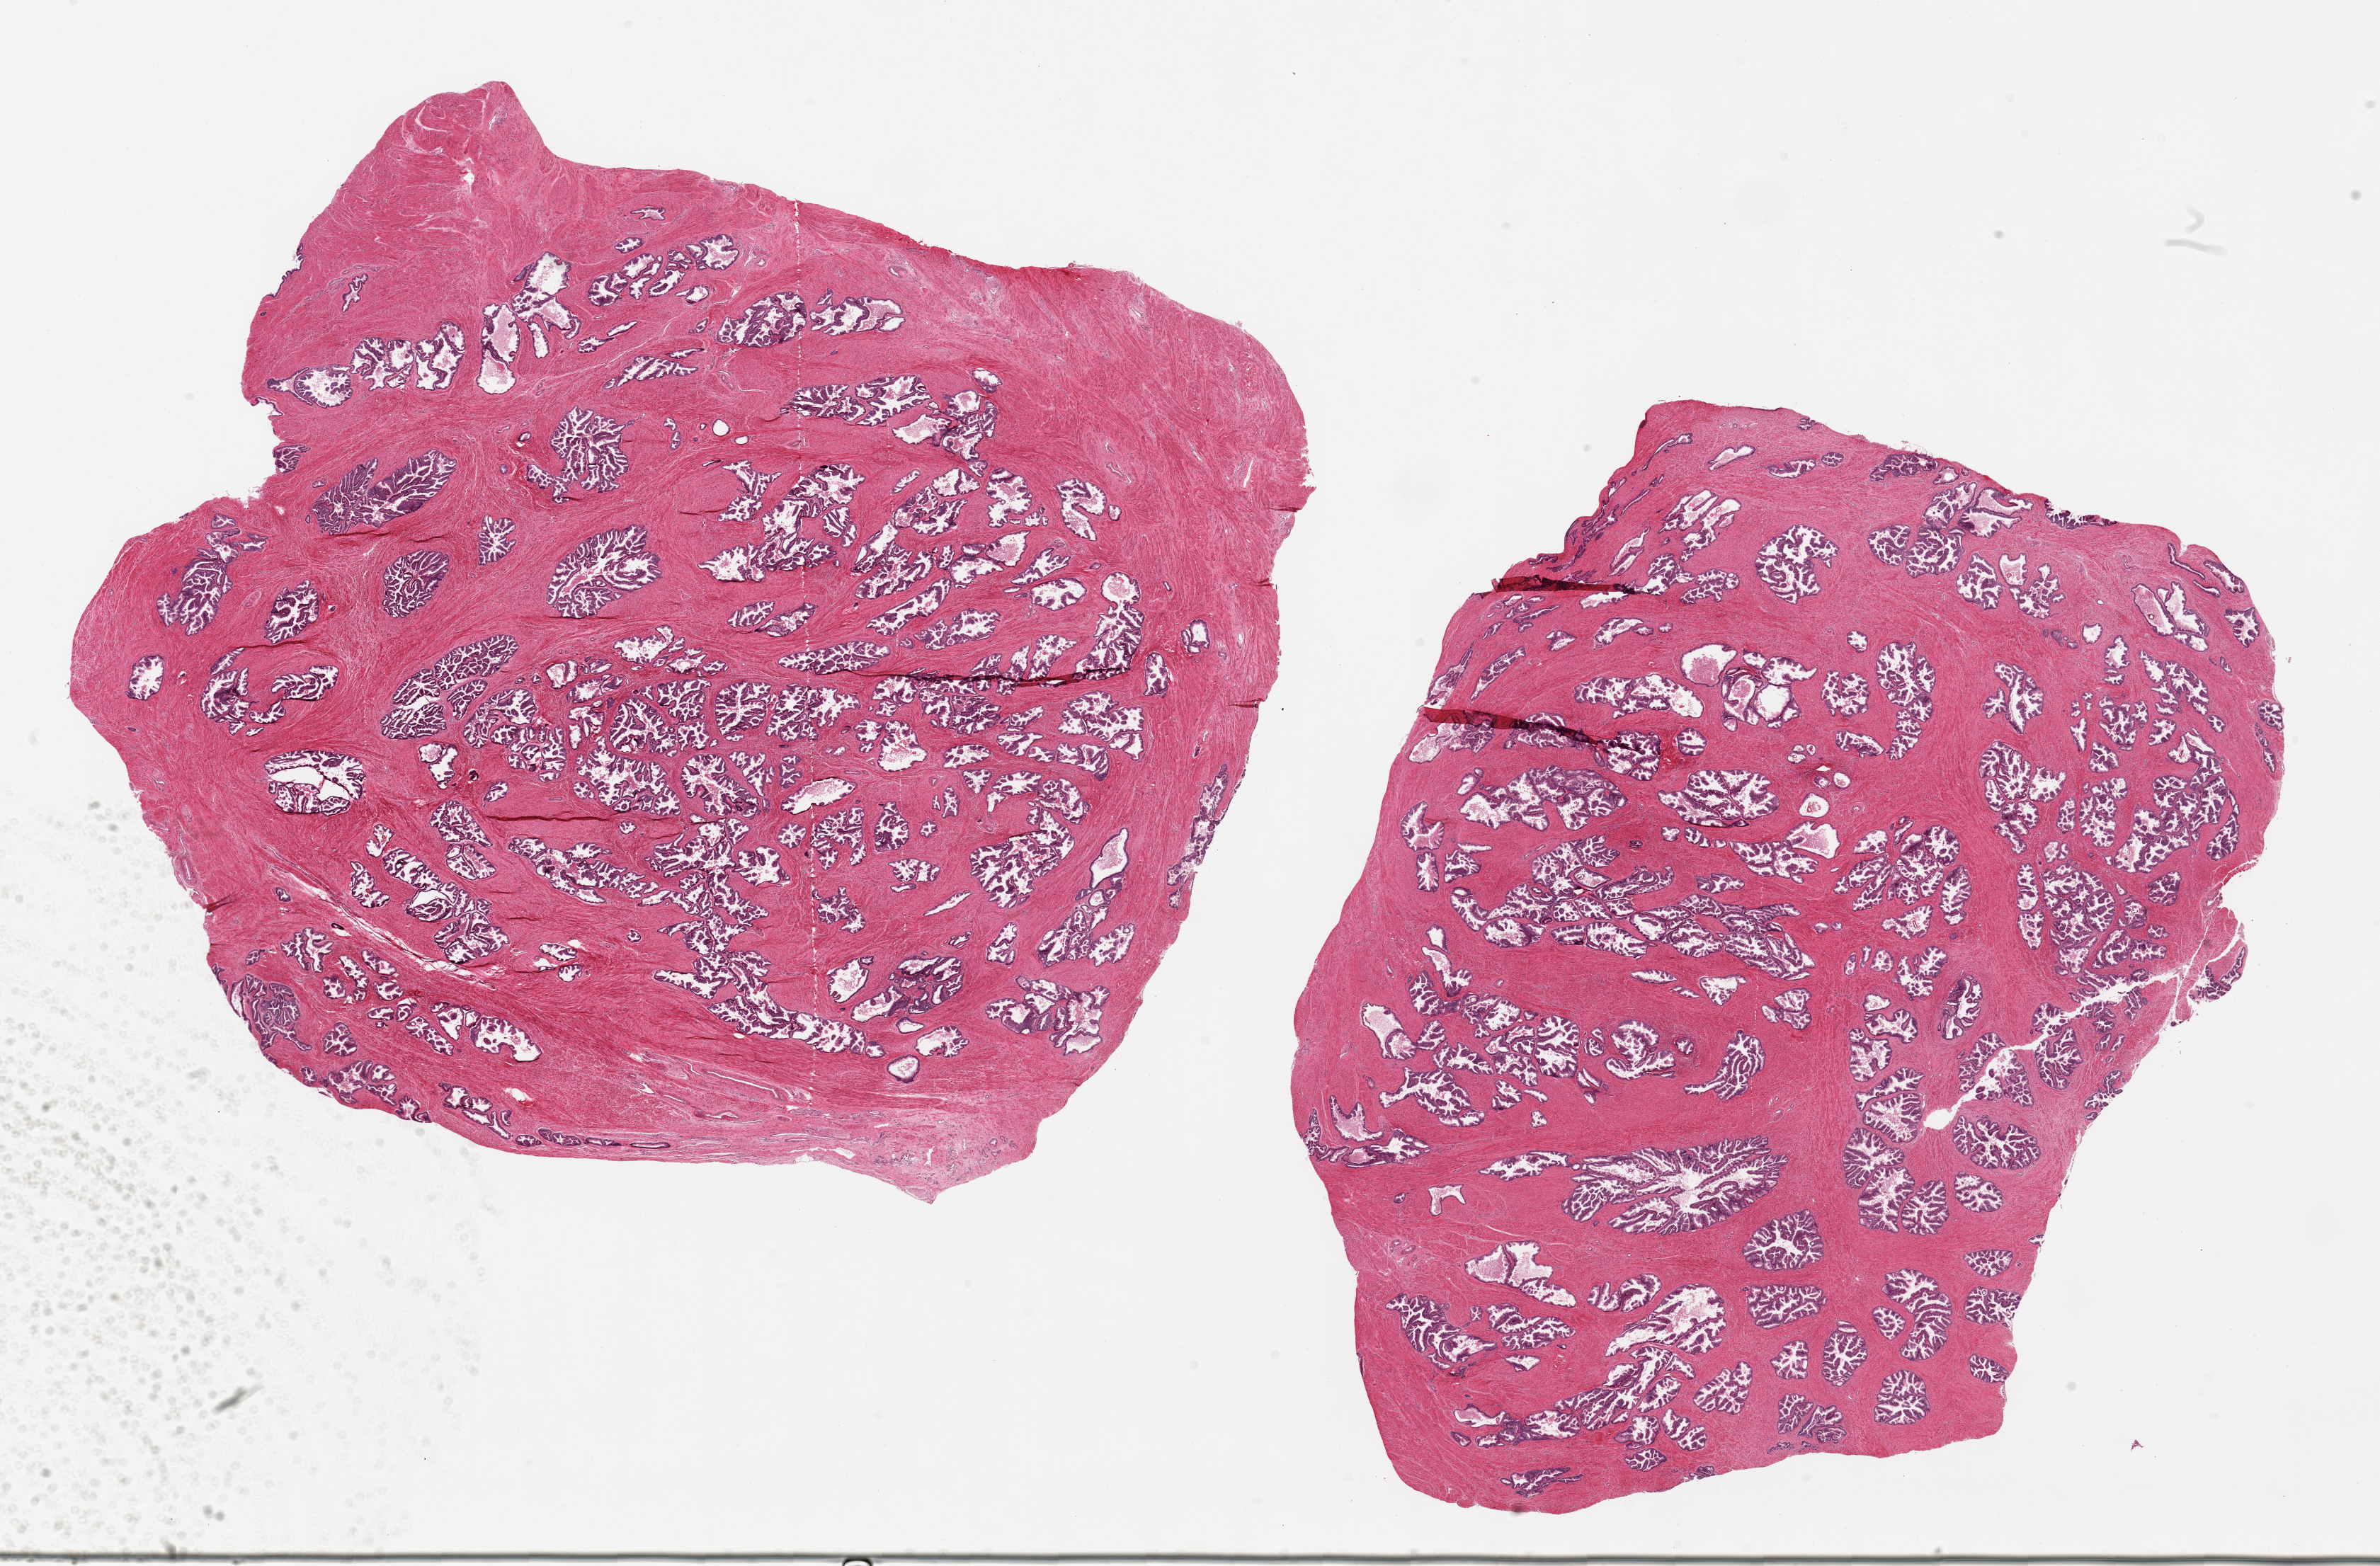
H&E whole-slide image, brightfield — low-resolution overview of the scanned area, about 26.6 x 17.5 mm; PAXgene-fixed, paraffin-embedded tissue; section of prostate (target tissue); donor tissue sample.
Reviewer comment on this tissue sample: 2 pieces; fibromuscular stroma admixed with glands.